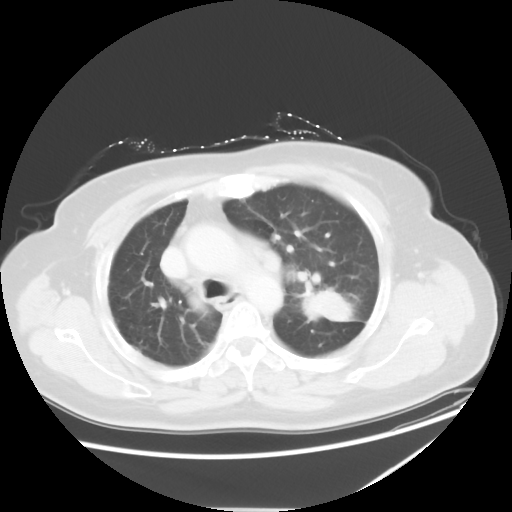
Chest CT, one axial slice. Position 39 of 54 along the scan axis. Reconstruction kernel STANDARD. Lung window (W 1500 / L -600 HU). 5 mm slice thickness. 512 × 512 image matrix, field of view 384 × 384 mm. Female patient, age 61 years. Case-level facts recorded for this patient, not image findings: clinical TNM (as recorded): T1c N3 M1.
Annotated regions visible in this slice (rectangle marked by the reading radiologist):
- lung tumour (recorded histology: adenocarcinoma): bounding box [x1, y1, x2, y2] px = [297, 286, 362, 328]